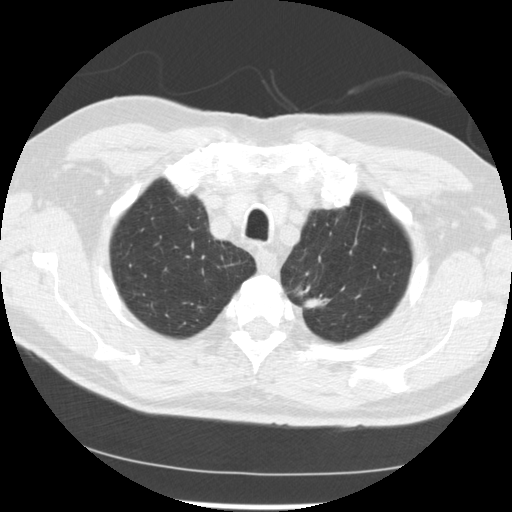
Low-dose screening chest CT, one axial slice. Reconstruction kernel STANDARD. Lung window (W 1500 / L -600 HU). 2.5 mm slice thickness. 512 × 512 image matrix.
Outlined on this slice (manually delineated by an expert):
- lesion 2 (tumor, upper lobe of left lung): bounding box (x1, y1, x2, y2) in pixels: (305, 298, 328, 308)